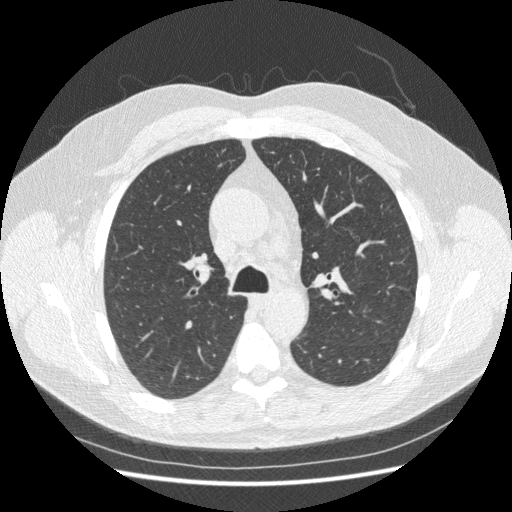
Chest CT (low-dose screening protocol), one axial image; first (baseline) screen; lung window (W 1500 / L -600 HU); standard (soft-tissue) reconstruction kernel (STANDARD); slice 89 of 250 in the series; 512 × 512 image matrix, field of view 360 × 360 mm. Male, age 63 years at enrolment. Current smoker at enrolment.
Expert-annotated lung lesion, box from (x=168, y=177) to (x=186, y=196) px. The exam's reader record, not a measurement of the box and not confirmed to be the same lesion: non-calcified nodule or mass ≥4 mm, right upper lobe, 5 × 4 mm, smooth margins, soft tissue attenuation. Participant outcome: lung cancer diagnosed 202 days after this screen — large cell carcinoma, NOS, right upper lobe, poorly differentiated (G3), stage IIIA (AJCC 6th edition), 15 mm at pathology.